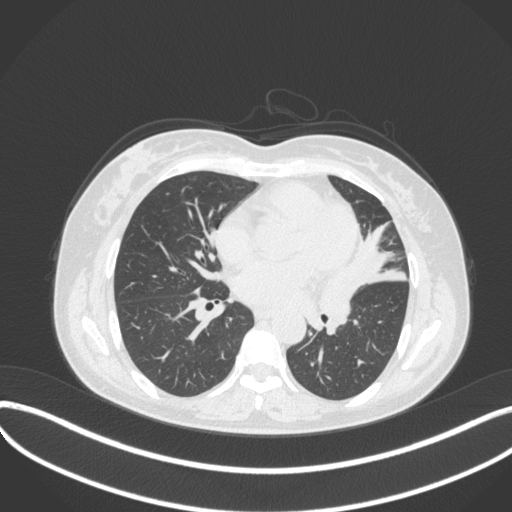
Chest CT, one axial slice; slice 167 of 373 in the series (ordered by position); reconstruction kernel B31f; 120 kVp; lung window (W 1500 / L -600 HU); 1 mm slice thickness; 512 × 512 image matrix, field of view 400 × 400 mm. Patient: female, 54 years. From the clinical record (not read from this slice): clinical TNM (as recorded): T2a N1 M0.
Structures marked on this image (bounding box drawn by a radiologist):
- lung tumour (recorded histology: small cell carcinoma): box from (x=316, y=266) to (x=367, y=333) px